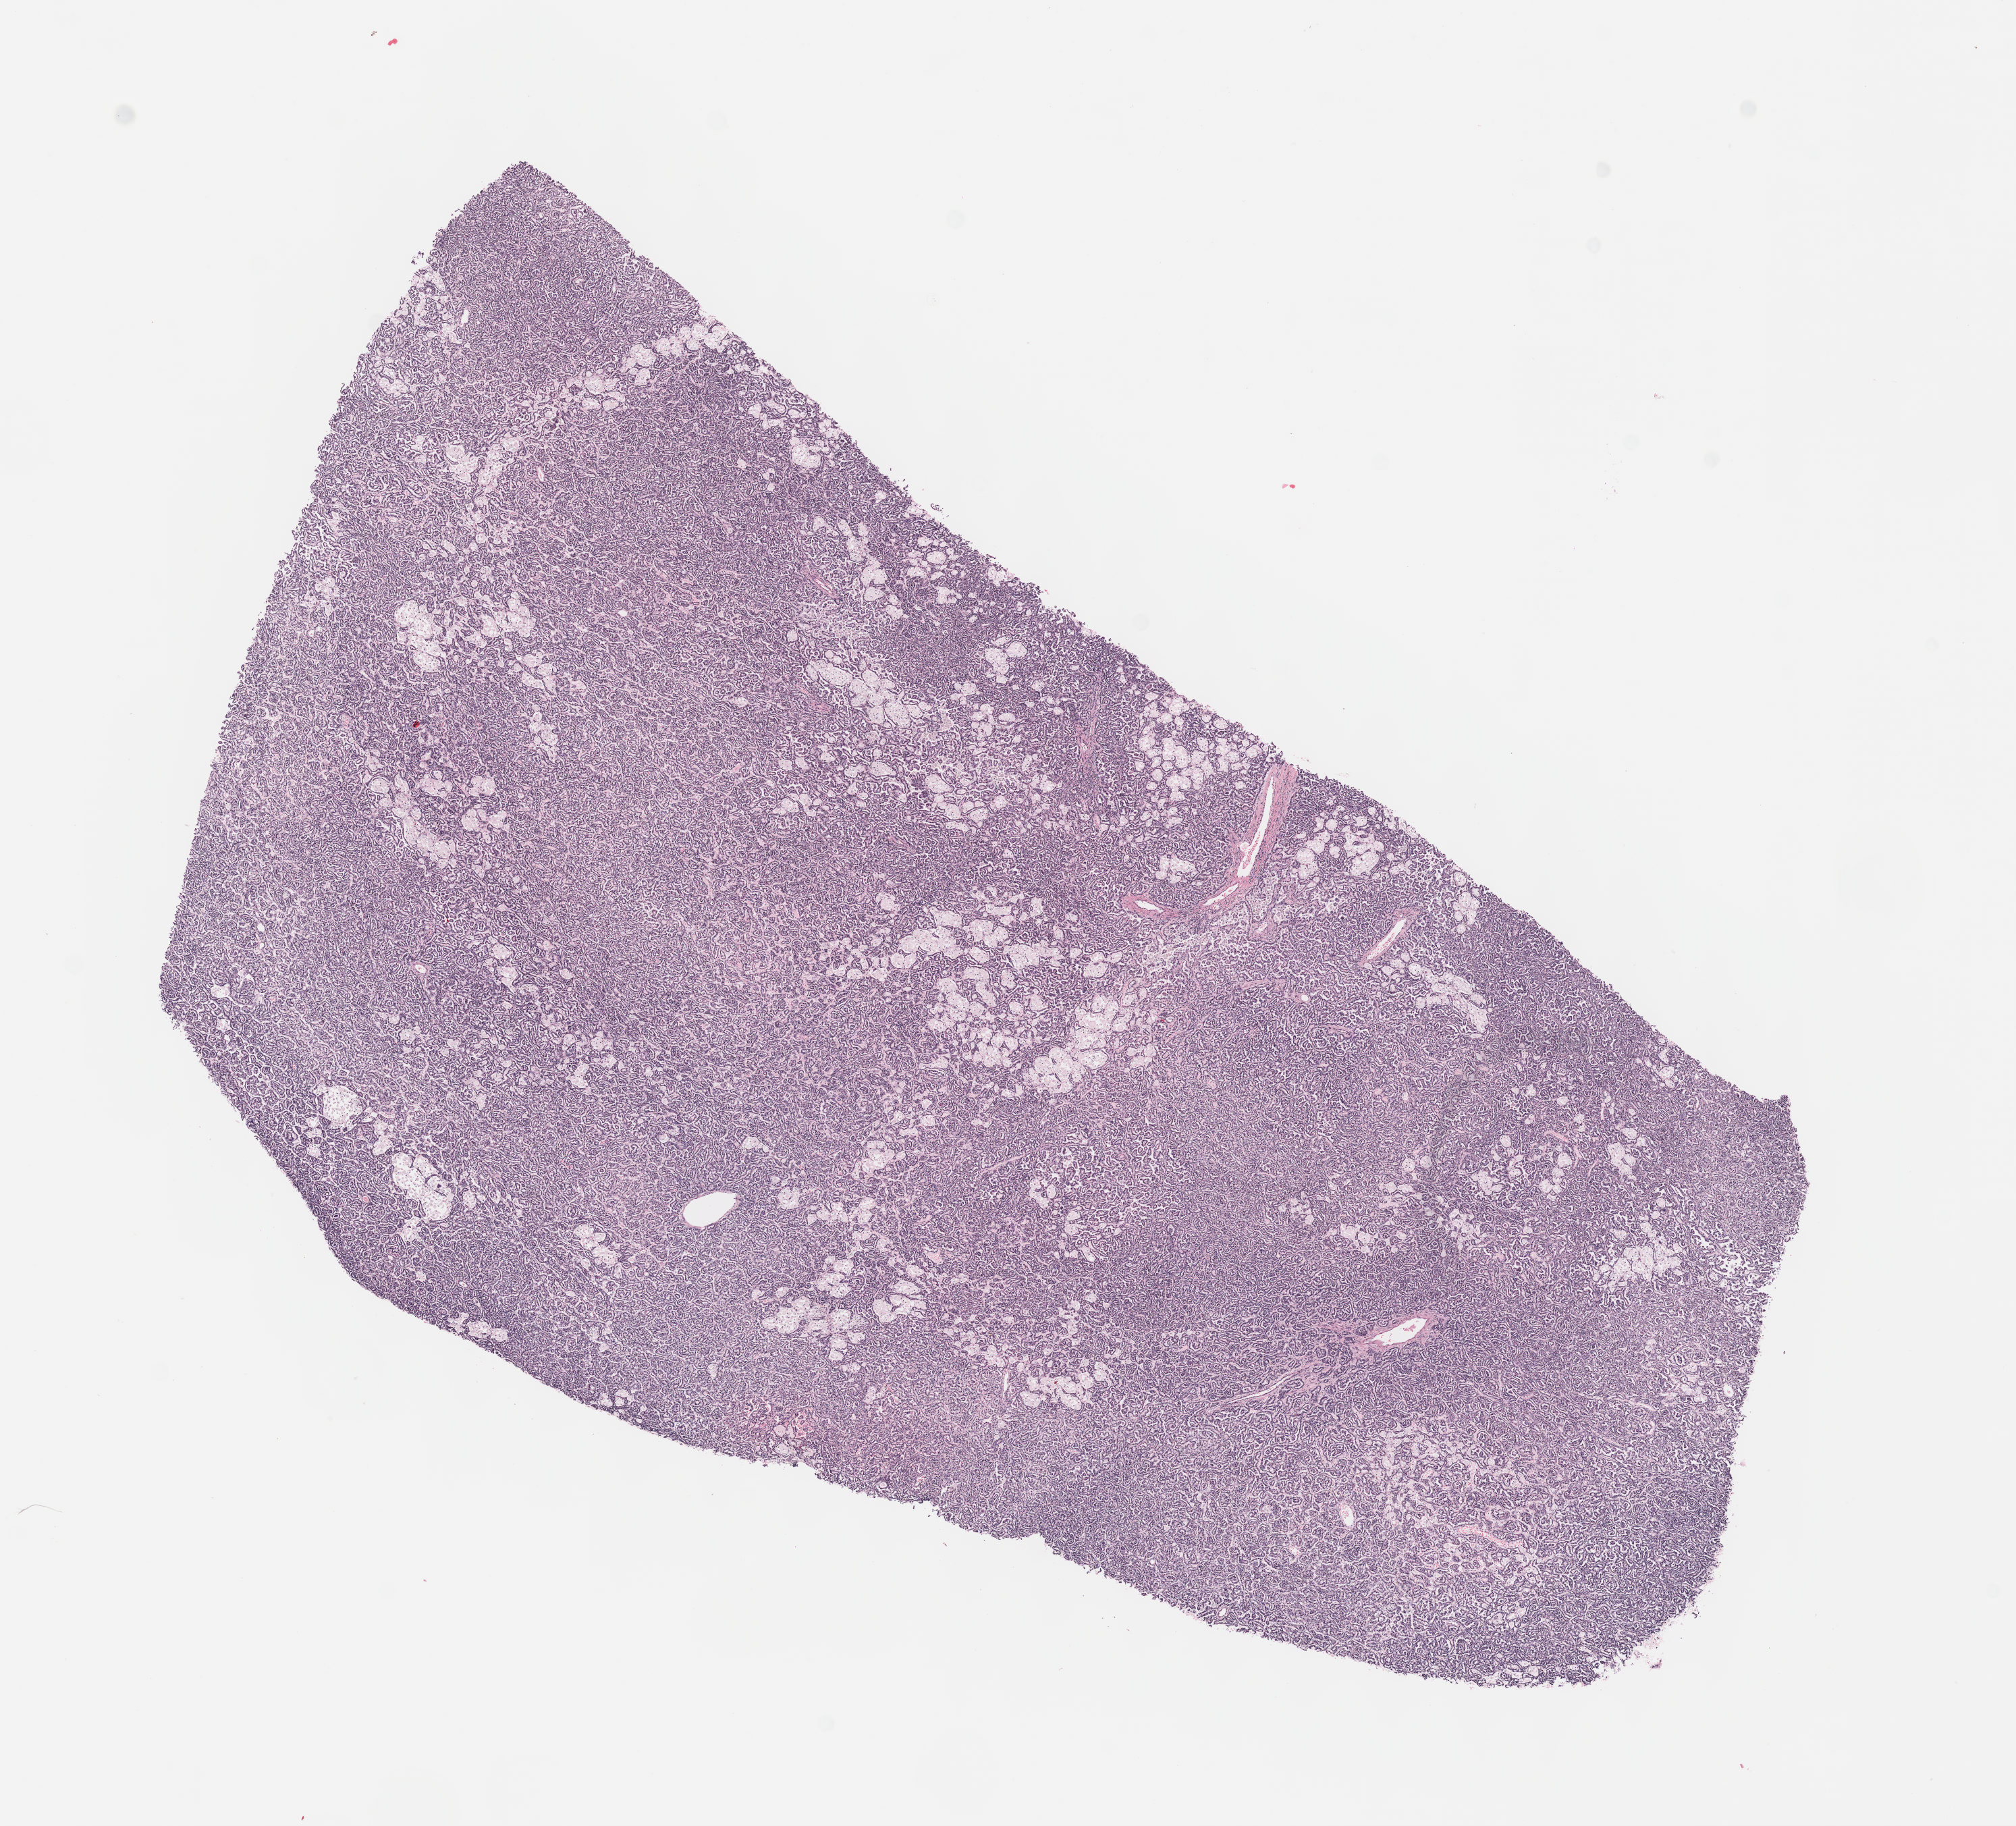
Hematoxylin and eosin (H&E) stained whole-slide image — a low-resolution overview of the entire scanned area, about 12.1 x 10.9 mm (acquisition: 40x scan), formalin-fixed paraffin-embedded (FFPE) diagnostic section, sample: primary tumour, kidney. Male patient; age at initial diagnosis 57 years.
Pathologic diagnosis: Papillary adenocarcinoma, NOS.